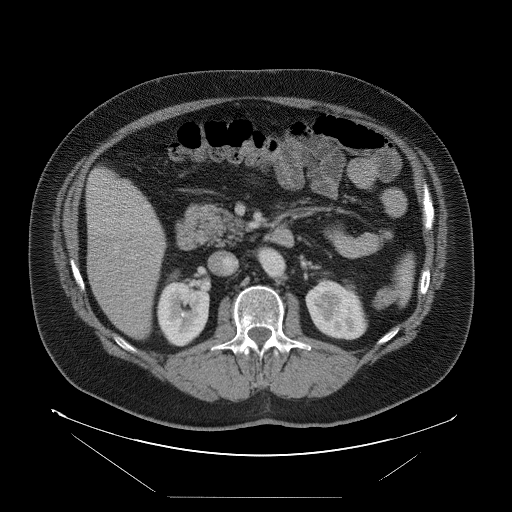
Contrast-enhanced abdominal CT, one axial slice. Slice 37 of 114 in the series (ordered by position). Soft-tissue window (W 400 / L 40 HU). 5 mm slice thickness. 512 × 512 image matrix, field of view 500 × 500 mm. Male patient, age 61 years. From the clinical record (not read from this slice): diagnosis: colorectal cancer liver metastases, imaged before liver resection; multiple liver metastases: no; largest metastasis: 6.5 cm; chemotherapy before resection: no.
Structures marked on this image (expert manual segmentation):
- liver: box from (x=88, y=169) to (x=166, y=339) px